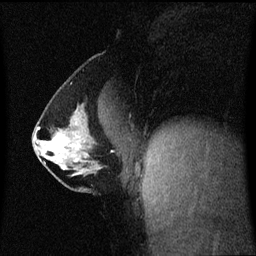
Breast MRI (dynamic contrast-enhanced), one sagittal slice. Position 29 of 60 along the scan axis. Dynamic contrast-enhanced series, image 2 of 3 at this slice position (ordered by acquisition). 1.5 T. TE 4.2 ms, TR 8.4 ms. 2 mm slice thickness. 256 × 256 image matrix. Patient: female, 40 years. From the clinical record (not read from this slice): setting: breast cancer imaged before/during neoadjuvant chemotherapy; receptor status: triple-negative.
Structures marked on this image (semi-automatically segmented with operator editing):
- analysis volume of interest (the breast-tissue region the enhancement analysis was run in; not a lesion): bounding box <33,112,112,188> (left, top, right, bottom; pixels)
- tumour enhancement mask (voxels above the 70 % enhancement threshold inside the analysis volume of interest): <39,128,78,162>